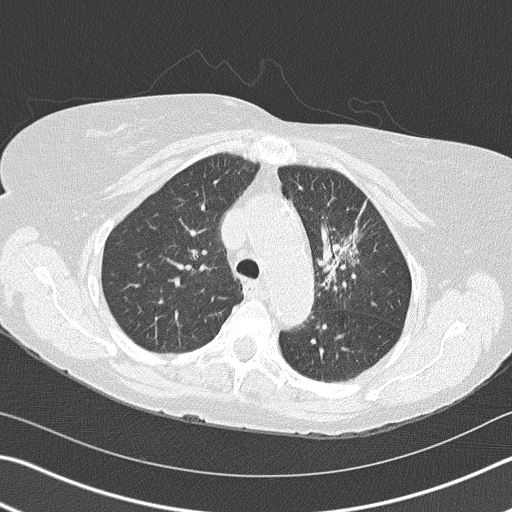
Axial slice from a low-dose chest CT screening exam. Second annual screen. Lung window (W 1500 / L -600 HU). 2 mm slice thickness. Lung (sharp) reconstruction kernel (B50f). Slice 114 of 153 in the series. 512 × 512 image matrix. Female participant, aged 68 years at enrolment.
Lesion marked by an expert reader, bounding box <294,197,392,311> (left, top, right, bottom; pixels). Screening reader's record for this exam (one nodule recorded; not confirmed to be the boxed lesion): non-calcified nodule or mass ≥4 mm, left upper lobe, 4 × 2 mm, spiculated (stellate) margins, soft tissue attenuation, pre-existing on the prior screen: yes; interval growth: yes. Later outcome: lung cancer diagnosed 392 days after this screen (after the third annual screen) — adenocarcinoma, NOS, left upper lobe, poorly differentiated (G3), stage IB (AJCC 6th edition), 50 mm at pathology.